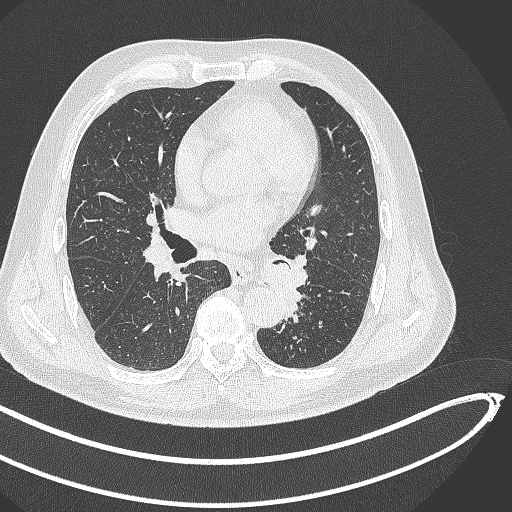
Chest CT, one axial slice. Slice 244 of 468 in the series (ordered by position). Reconstruction kernel B70f. Lung window (W 1500 / L -600 HU). 1 mm slice thickness. 512 × 512 image matrix, field of view 400 × 400 mm. Male patient, age 64 years. Case-level facts recorded for this patient, not image findings: clinical TNM (as recorded): T1c N0 M0; histopathological grade: G2.
Outlined on this slice (rectangle marked by the reading radiologist):
- lung tumour (recorded histology: squamous cell carcinoma): box from (x=257, y=261) to (x=305, y=311) px